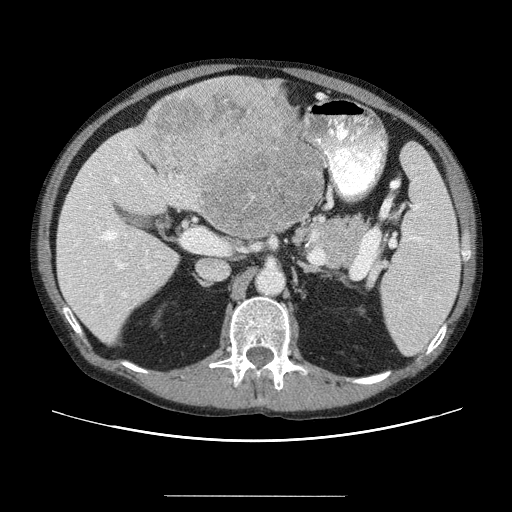
Contrast-enhanced abdominal CT (liver protocol), one axial slice; slice 21 of 69 in the series (ordered by position); soft-tissue window (W 400 / L 40 HU); 2.5 mm slice thickness; 512 × 512 image matrix, field of view 380 × 380 mm. Case-level facts recorded for this patient, not image findings: diagnosis: hepatocellular carcinoma (patient treated with transarterial chemoembolisation; whether this scan precedes or follows treatment is not stated here); TNM stage (as recorded): Stage-IVB; Child-Pugh class: B; tumour differentiation: poorly differentiated; tumour nodularity: multinodular.
Annotated regions visible in this slice (semi-automatic segmentation, software-assisted and operator-edited):
- liver parenchyma outside the tumour (the mass and vessels are separate outlines, so this box may not span the whole liver): bounding box [x1, y1, x2, y2] px = [56, 82, 310, 338]
- mass: [139, 79, 328, 242]
- liver vessels: [59, 150, 155, 318]